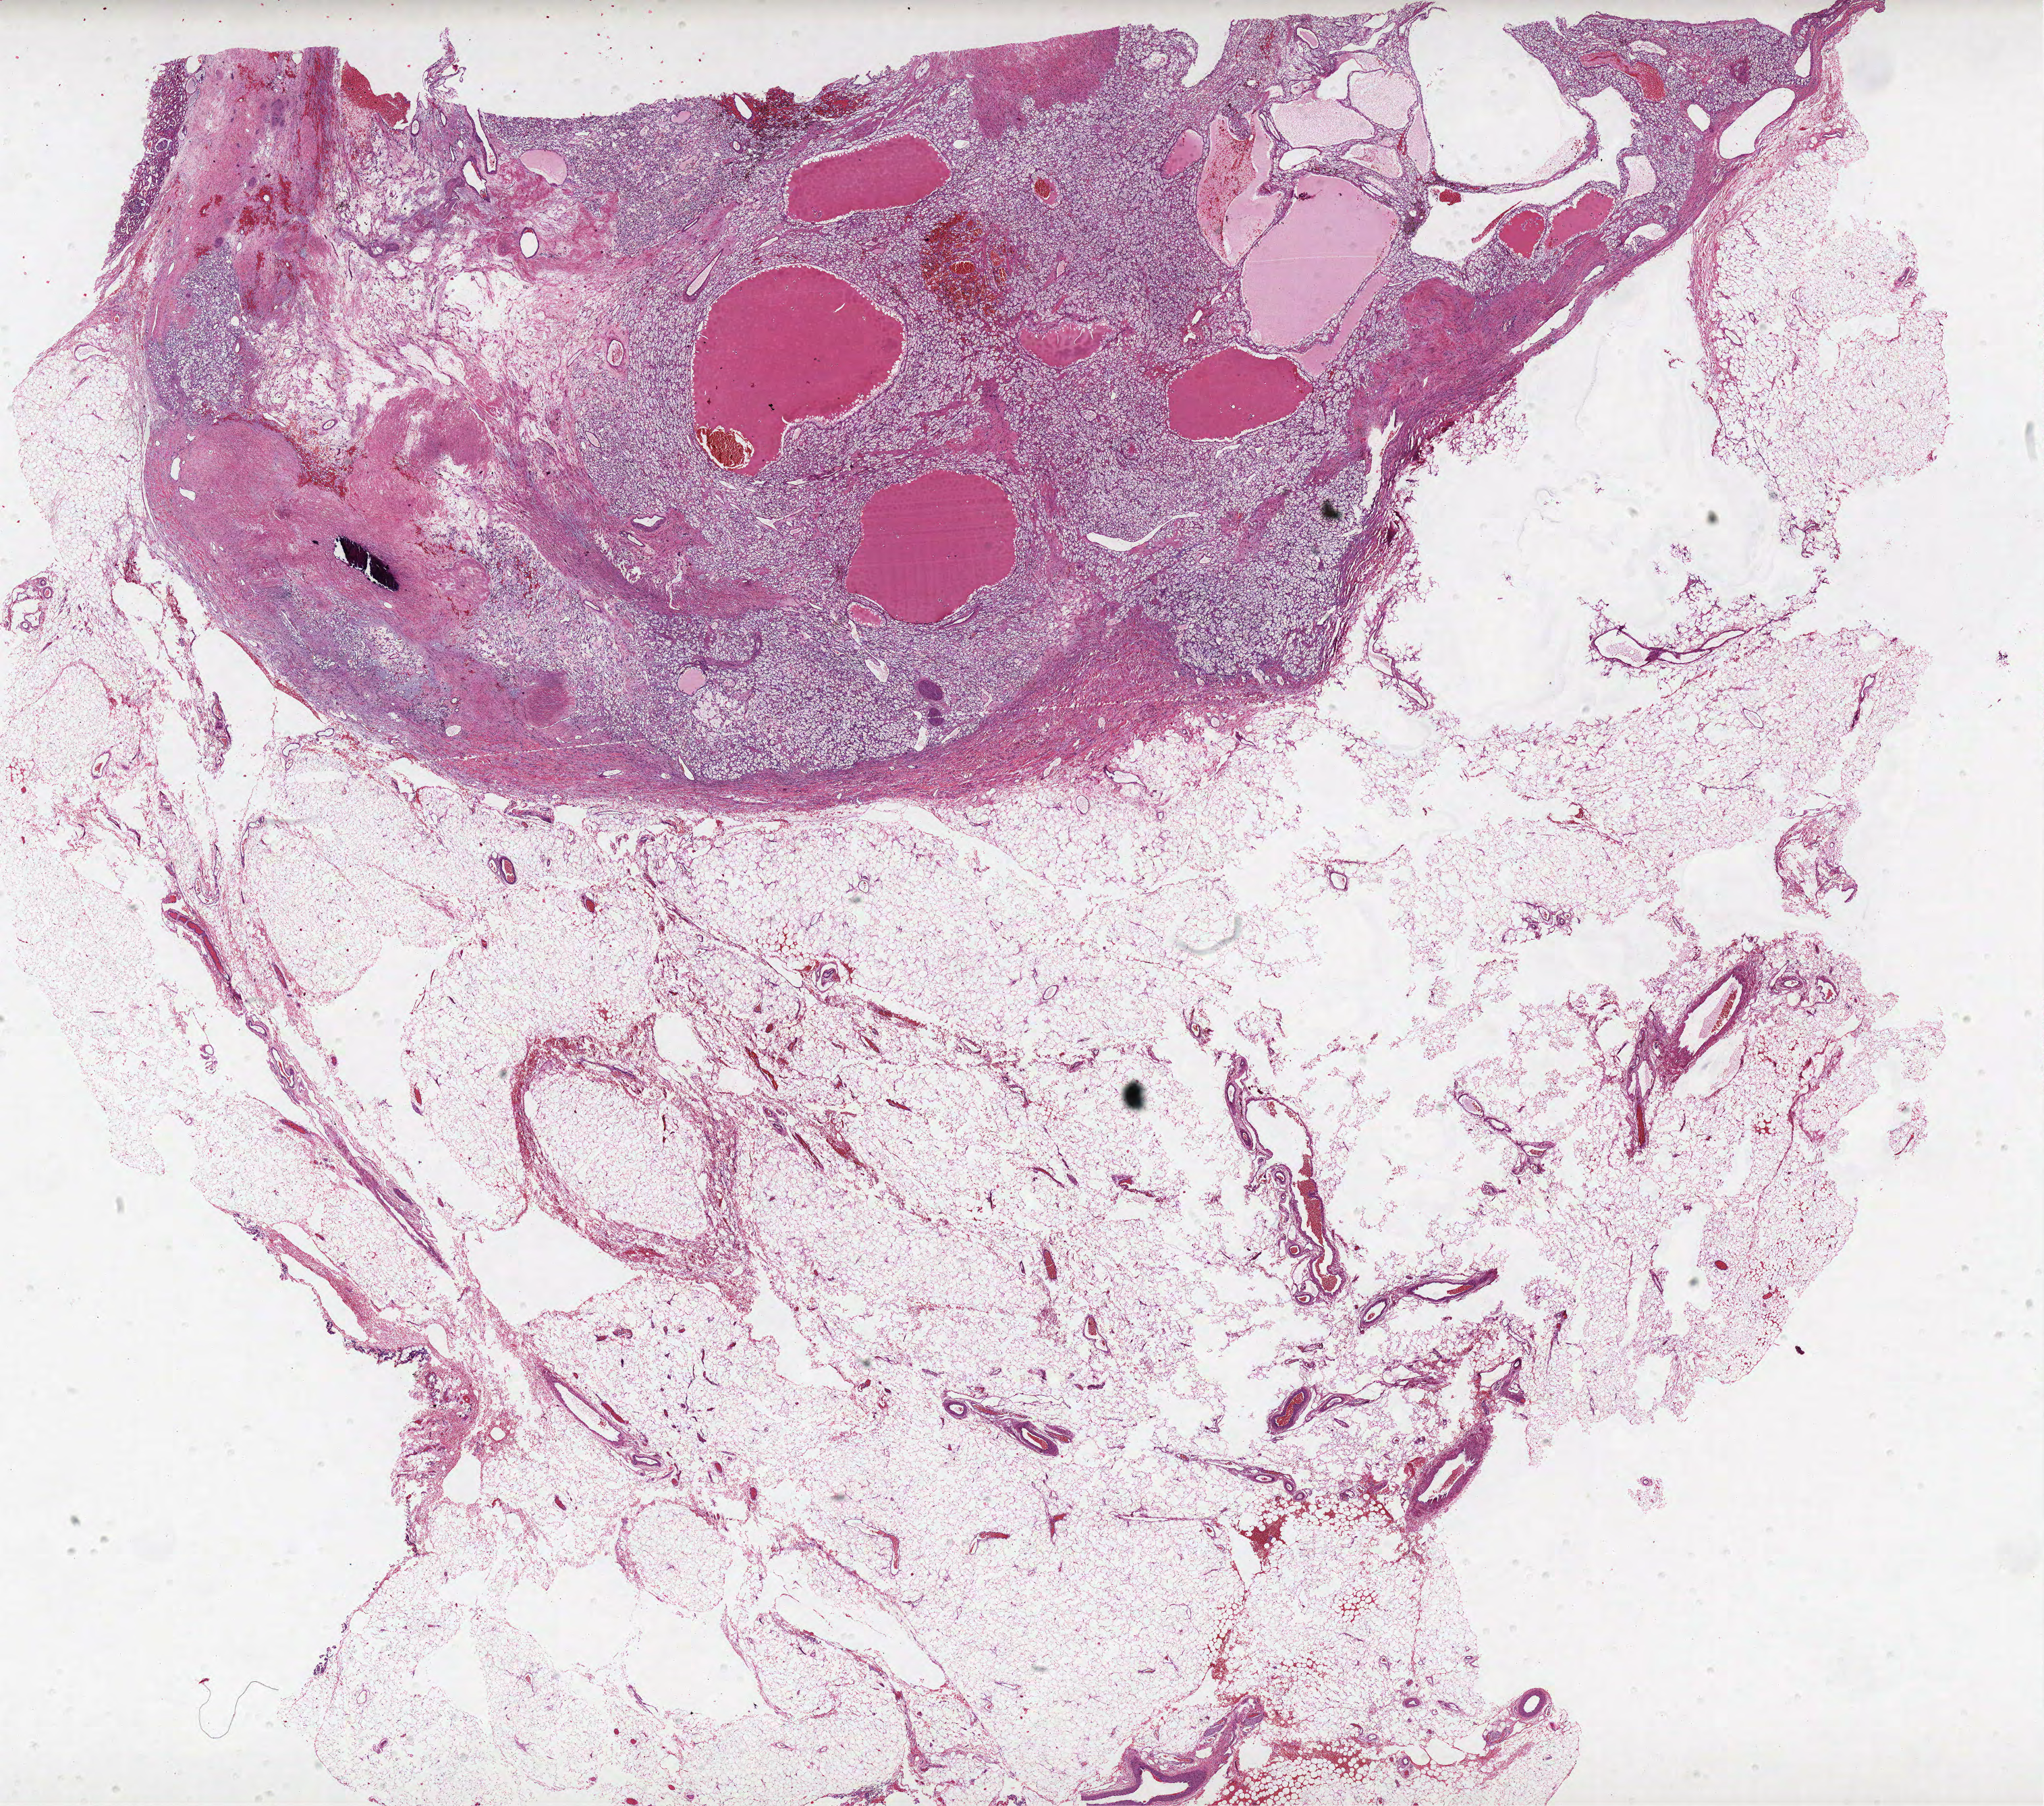
Digitized Hematoxylin and eosin (H&E) stained tissue section (whole slide), low-resolution overview of the scanned area, about 24.2 x 21.4 mm (acquisition: 40x scan). FFPE section. Primary tumour sample from the kidney. Male, age 57 years at initial diagnosis. Histologic grade: G2 (moderately differentiated).
• AJCC pathologic stage: I
• laterality: left
• histologic diagnosis: Clear cell adenocarcinoma, NOS